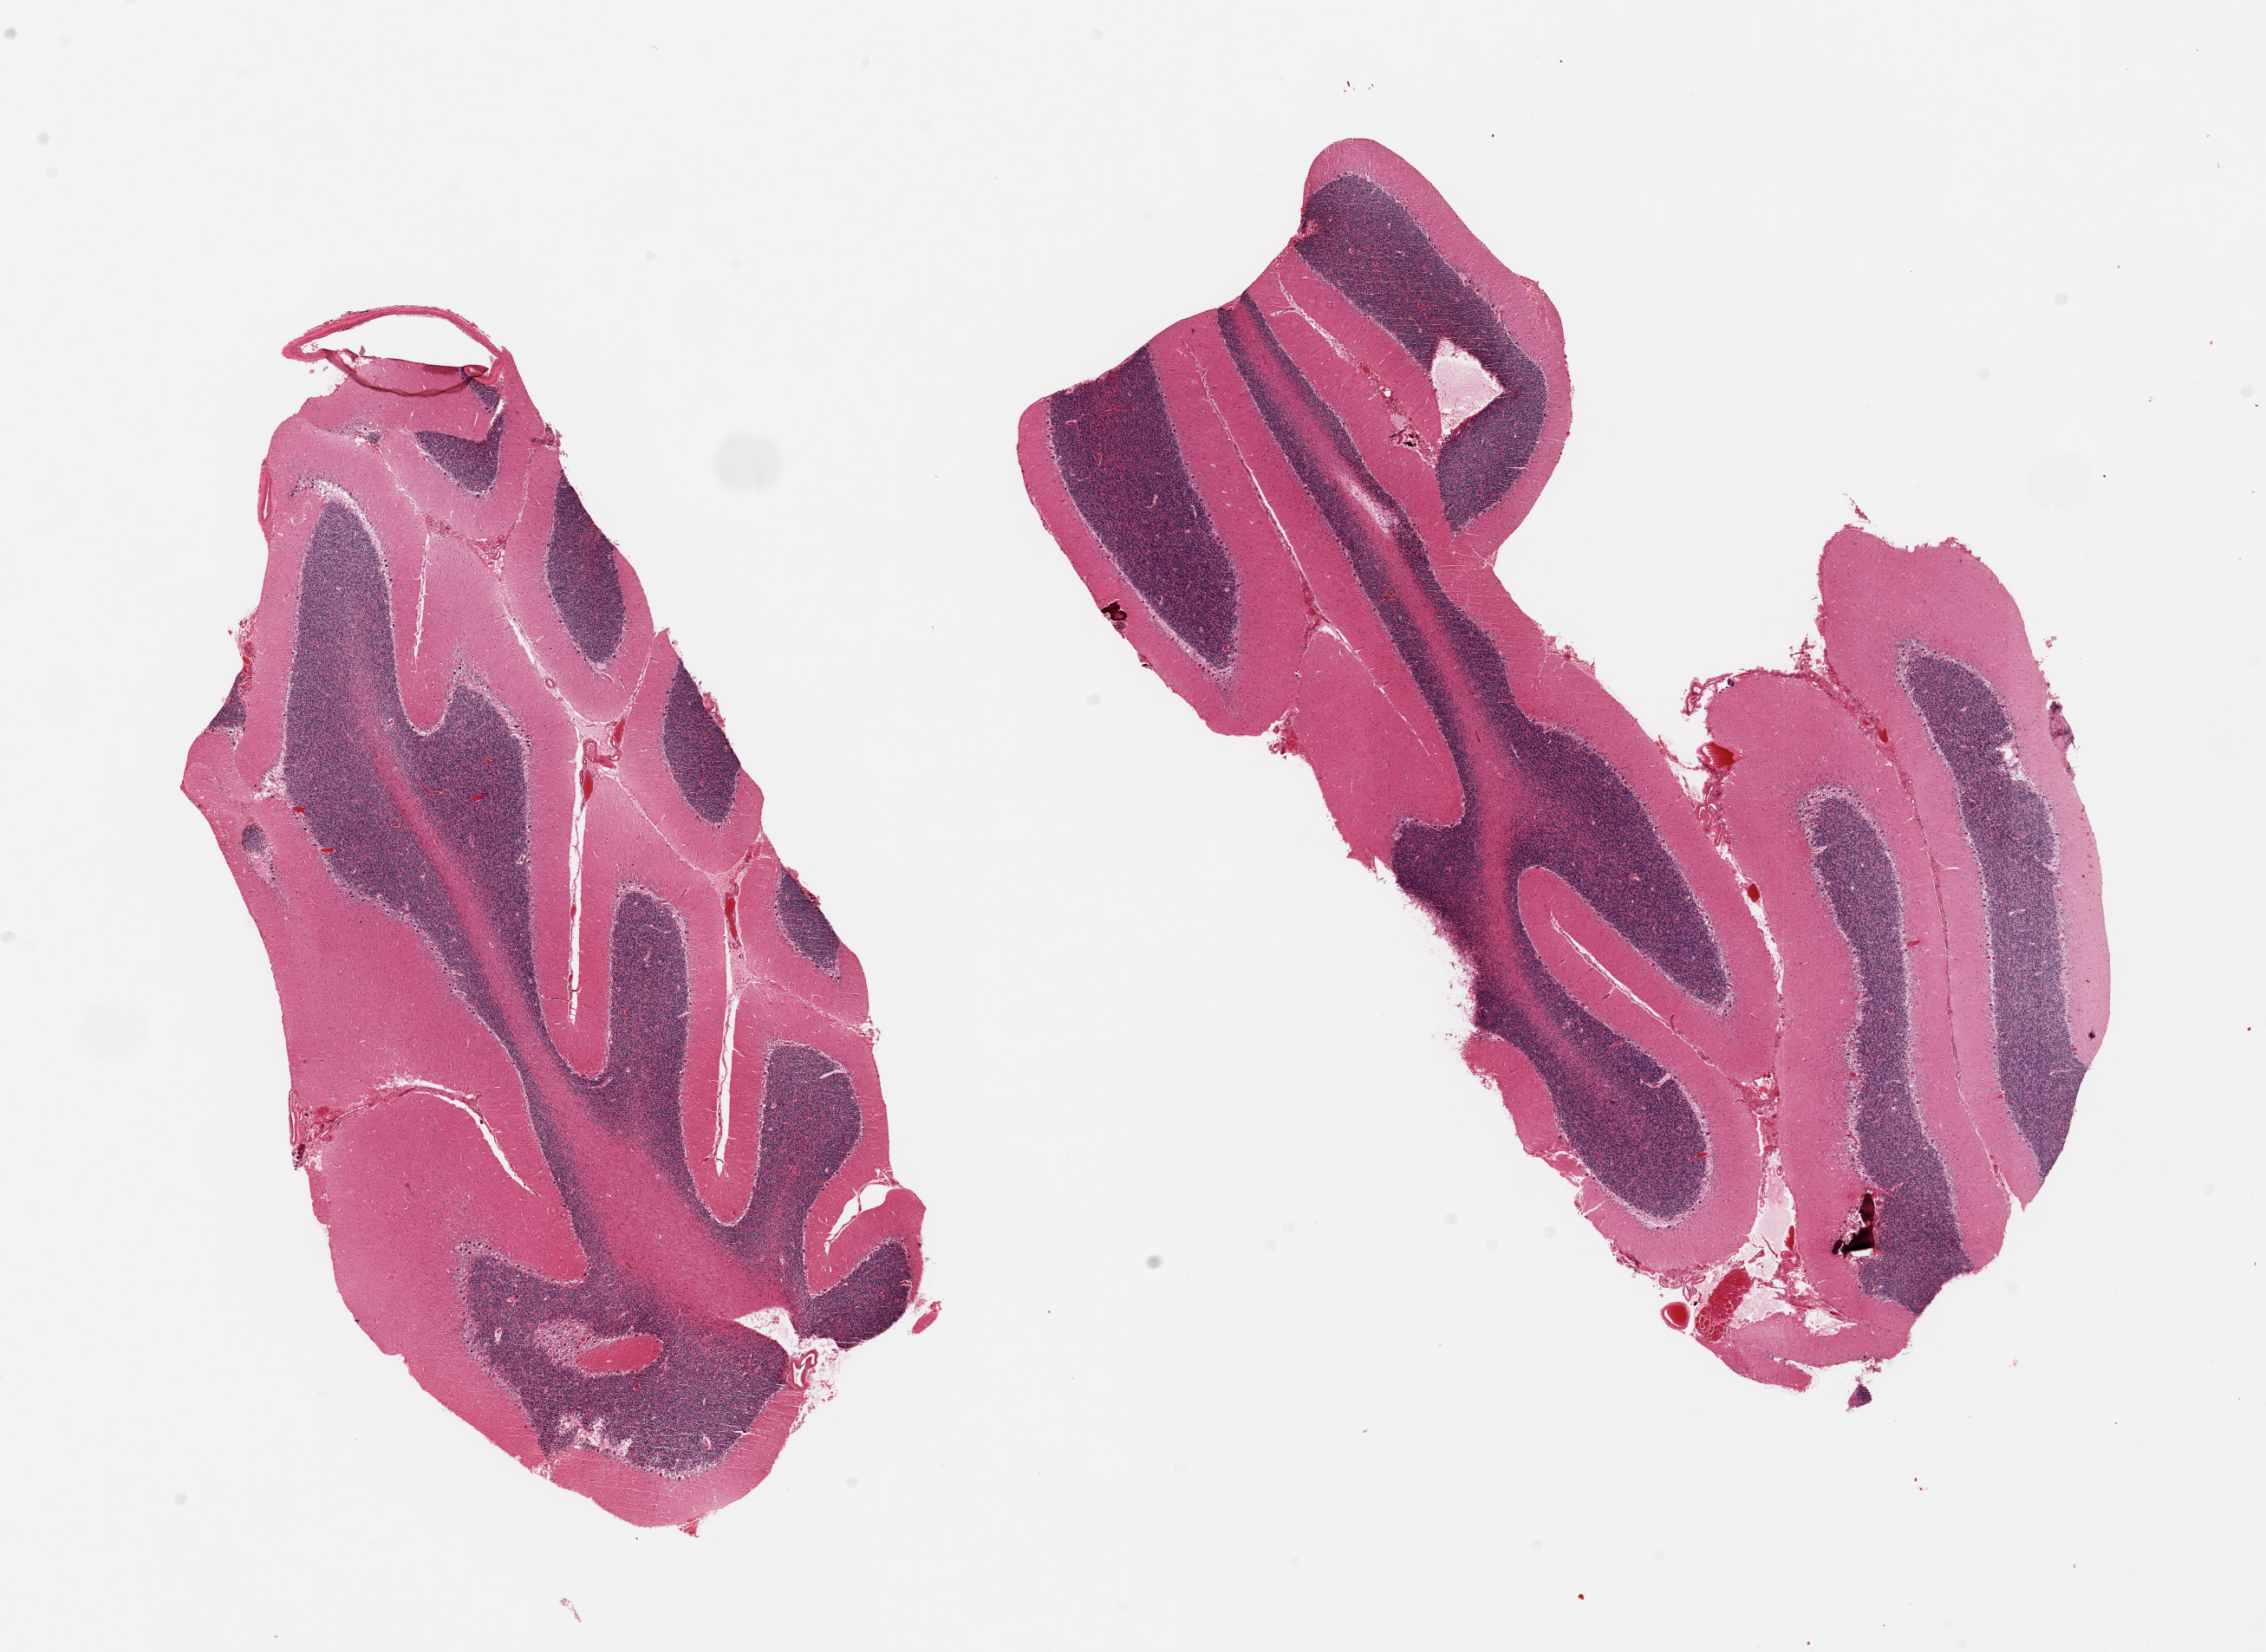
Digitized H&E-stained section, low-resolution overview of the scanned area, about 20.7 x 15.1 mm (acquisition: 20x scan), PAXgene-fixed, paraffin-embedded tissue, sampled site (target tissue): cerebellum, tissue donor sample.
Pathologist's review note for this sample: 2 pieces; Purkinje cells well visualized, fragment of skeletal muscle.